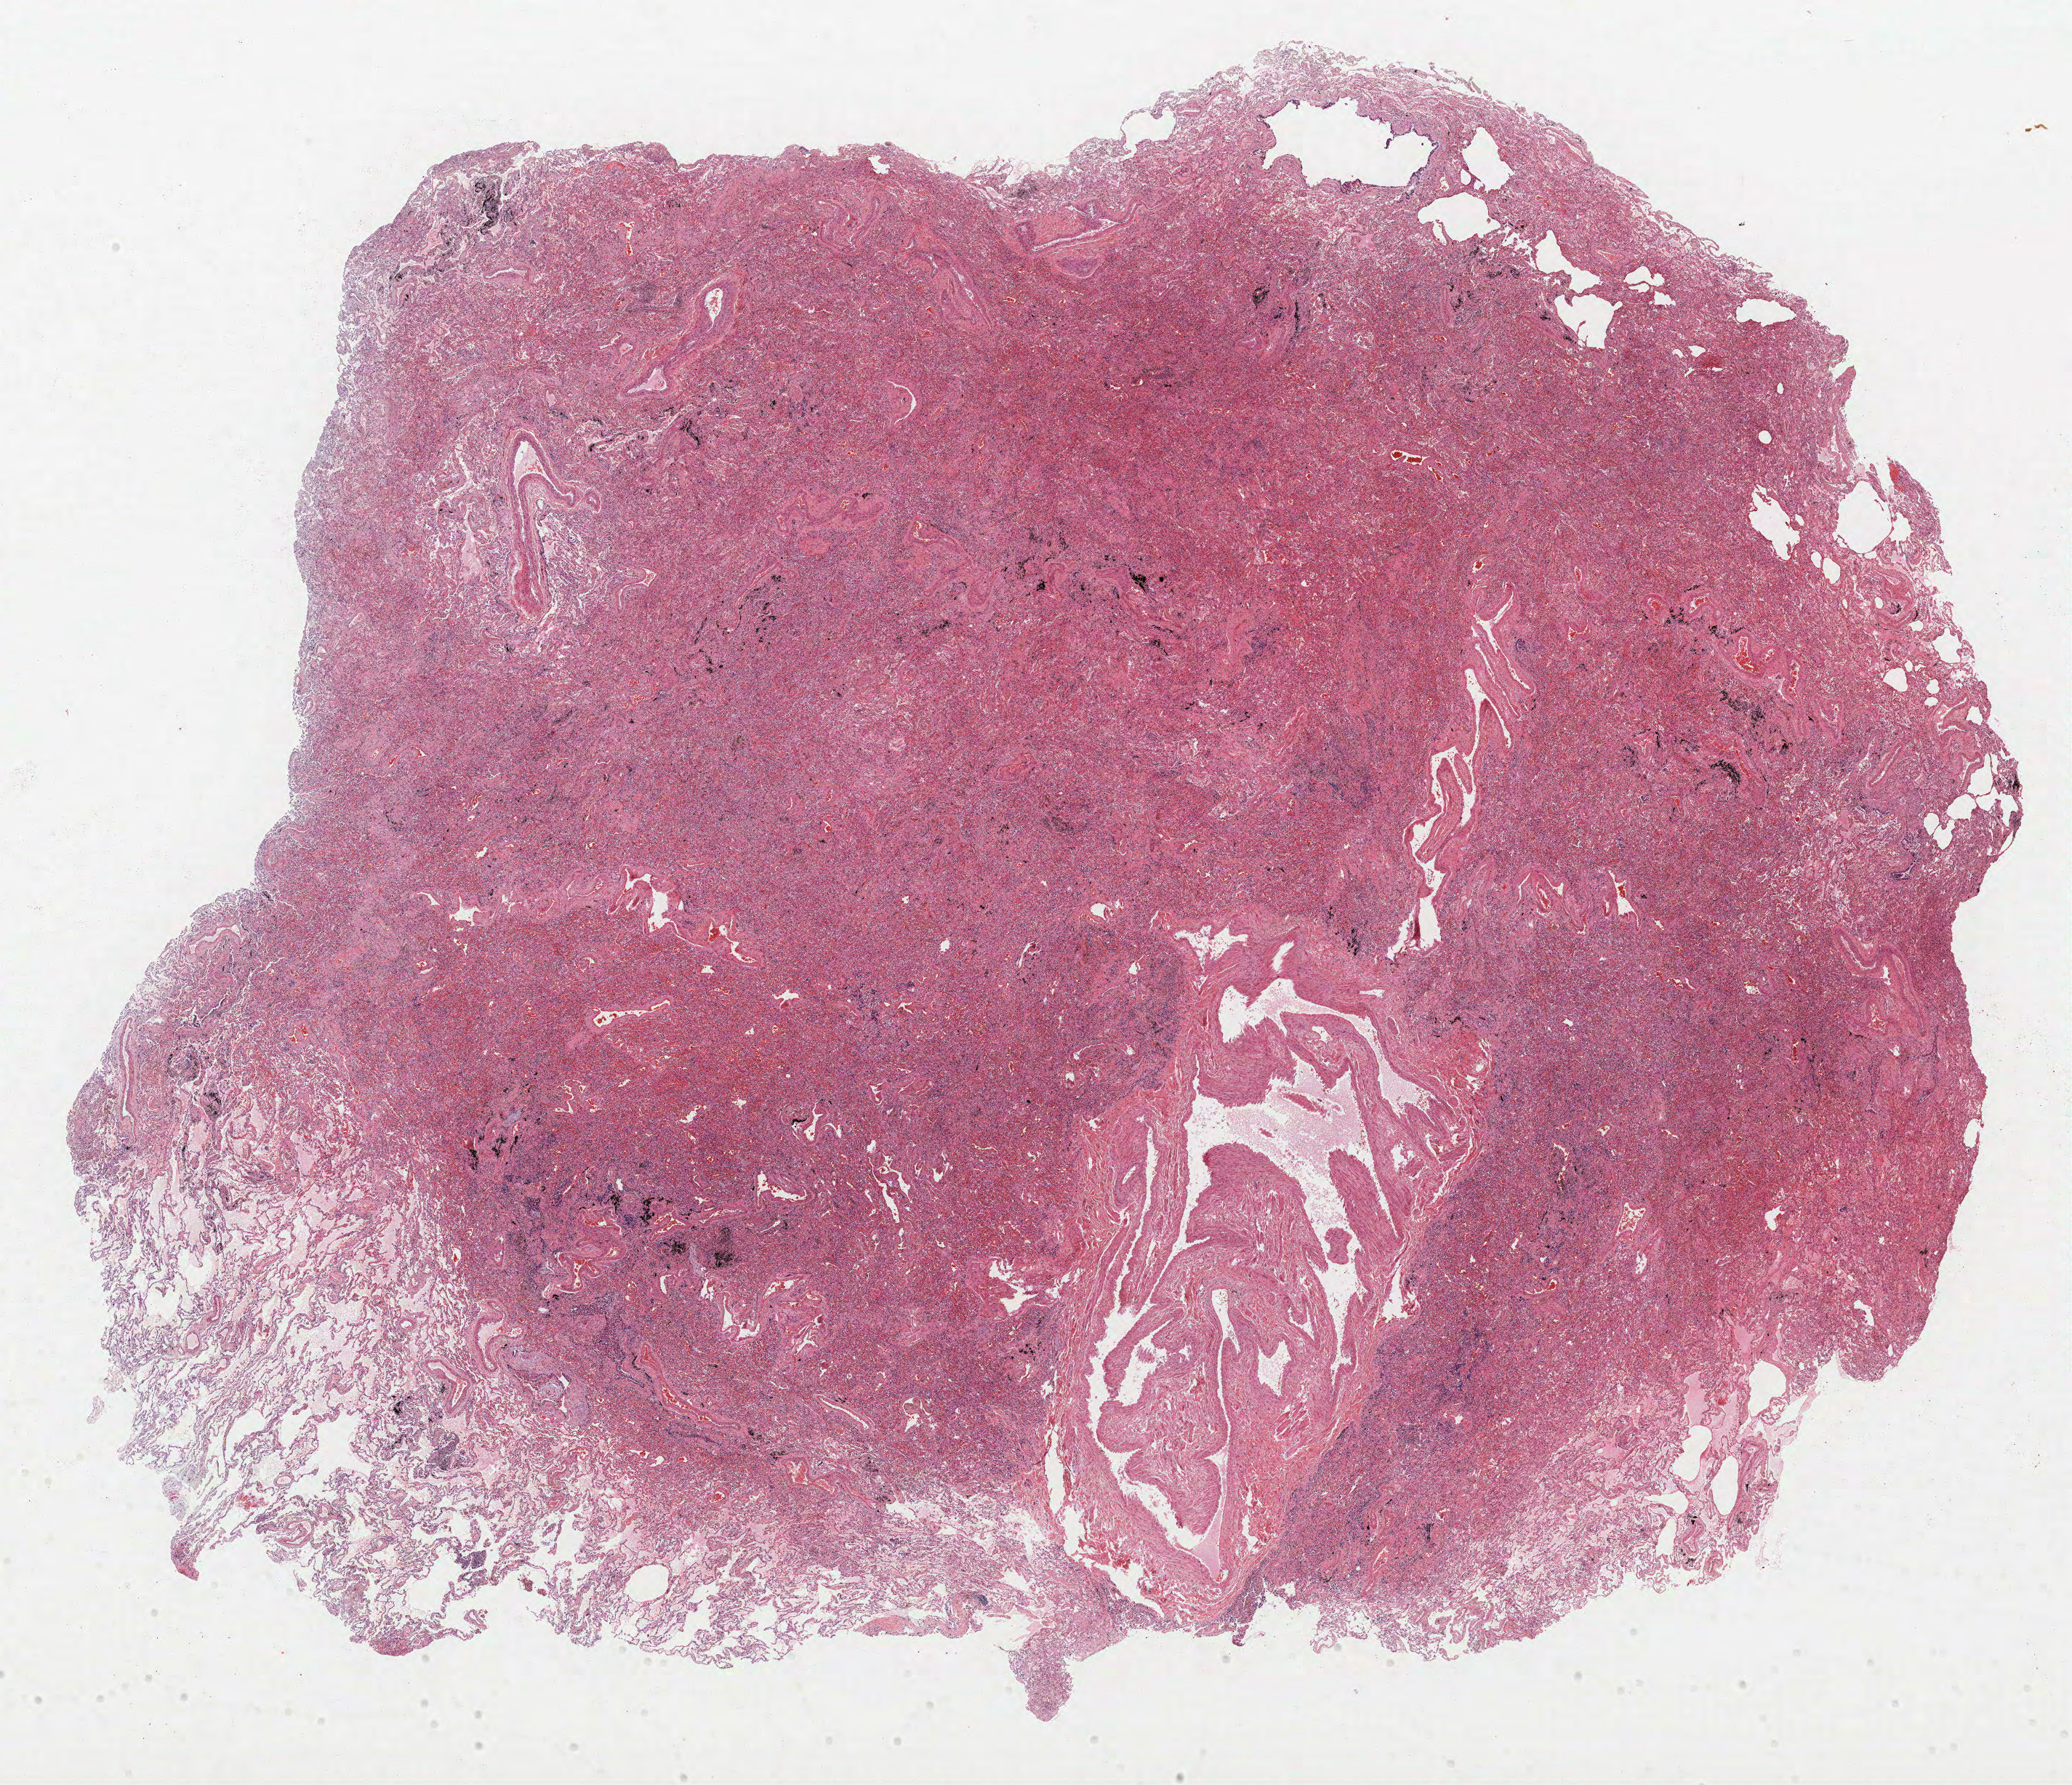
Whole-slide histology image, H&E — whole scanned area (about 22.8 x 19.6 mm, from a 40x scan) shown as a low-resolution overview. FFPE section. Lung. Male patient, aged 70 at enrolment. Current smoker at enrolment.
Participant's lung-cancer diagnosis: Mixed cell adenocarcinoma.